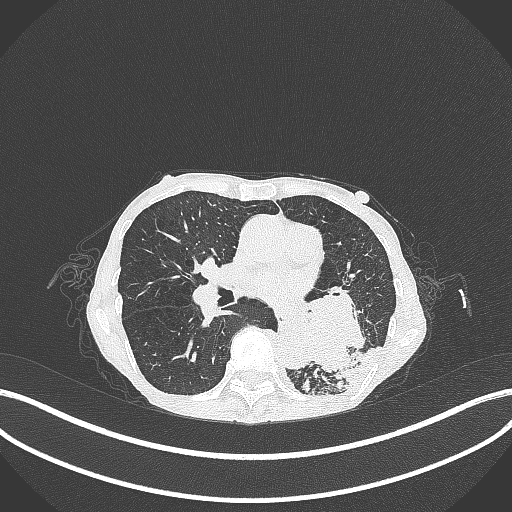
Chest CT, one axial slice. Position 137 of 347 along the scan axis. Reconstruction kernel B70f. Lung window (W 1500 / L -600 HU). 1 mm slice thickness. 512 × 512 image matrix. Patient: female, 70 years. From the clinical record (not read from this slice): clinical TNM (as recorded): T3 N0 M0; histopathological grade: G3.
Outlined on this slice (rectangle marked by the reading radiologist):
- lung tumour (recorded histology: small cell carcinoma): bounding box [x1, y1, x2, y2] px = [299, 282, 376, 383]